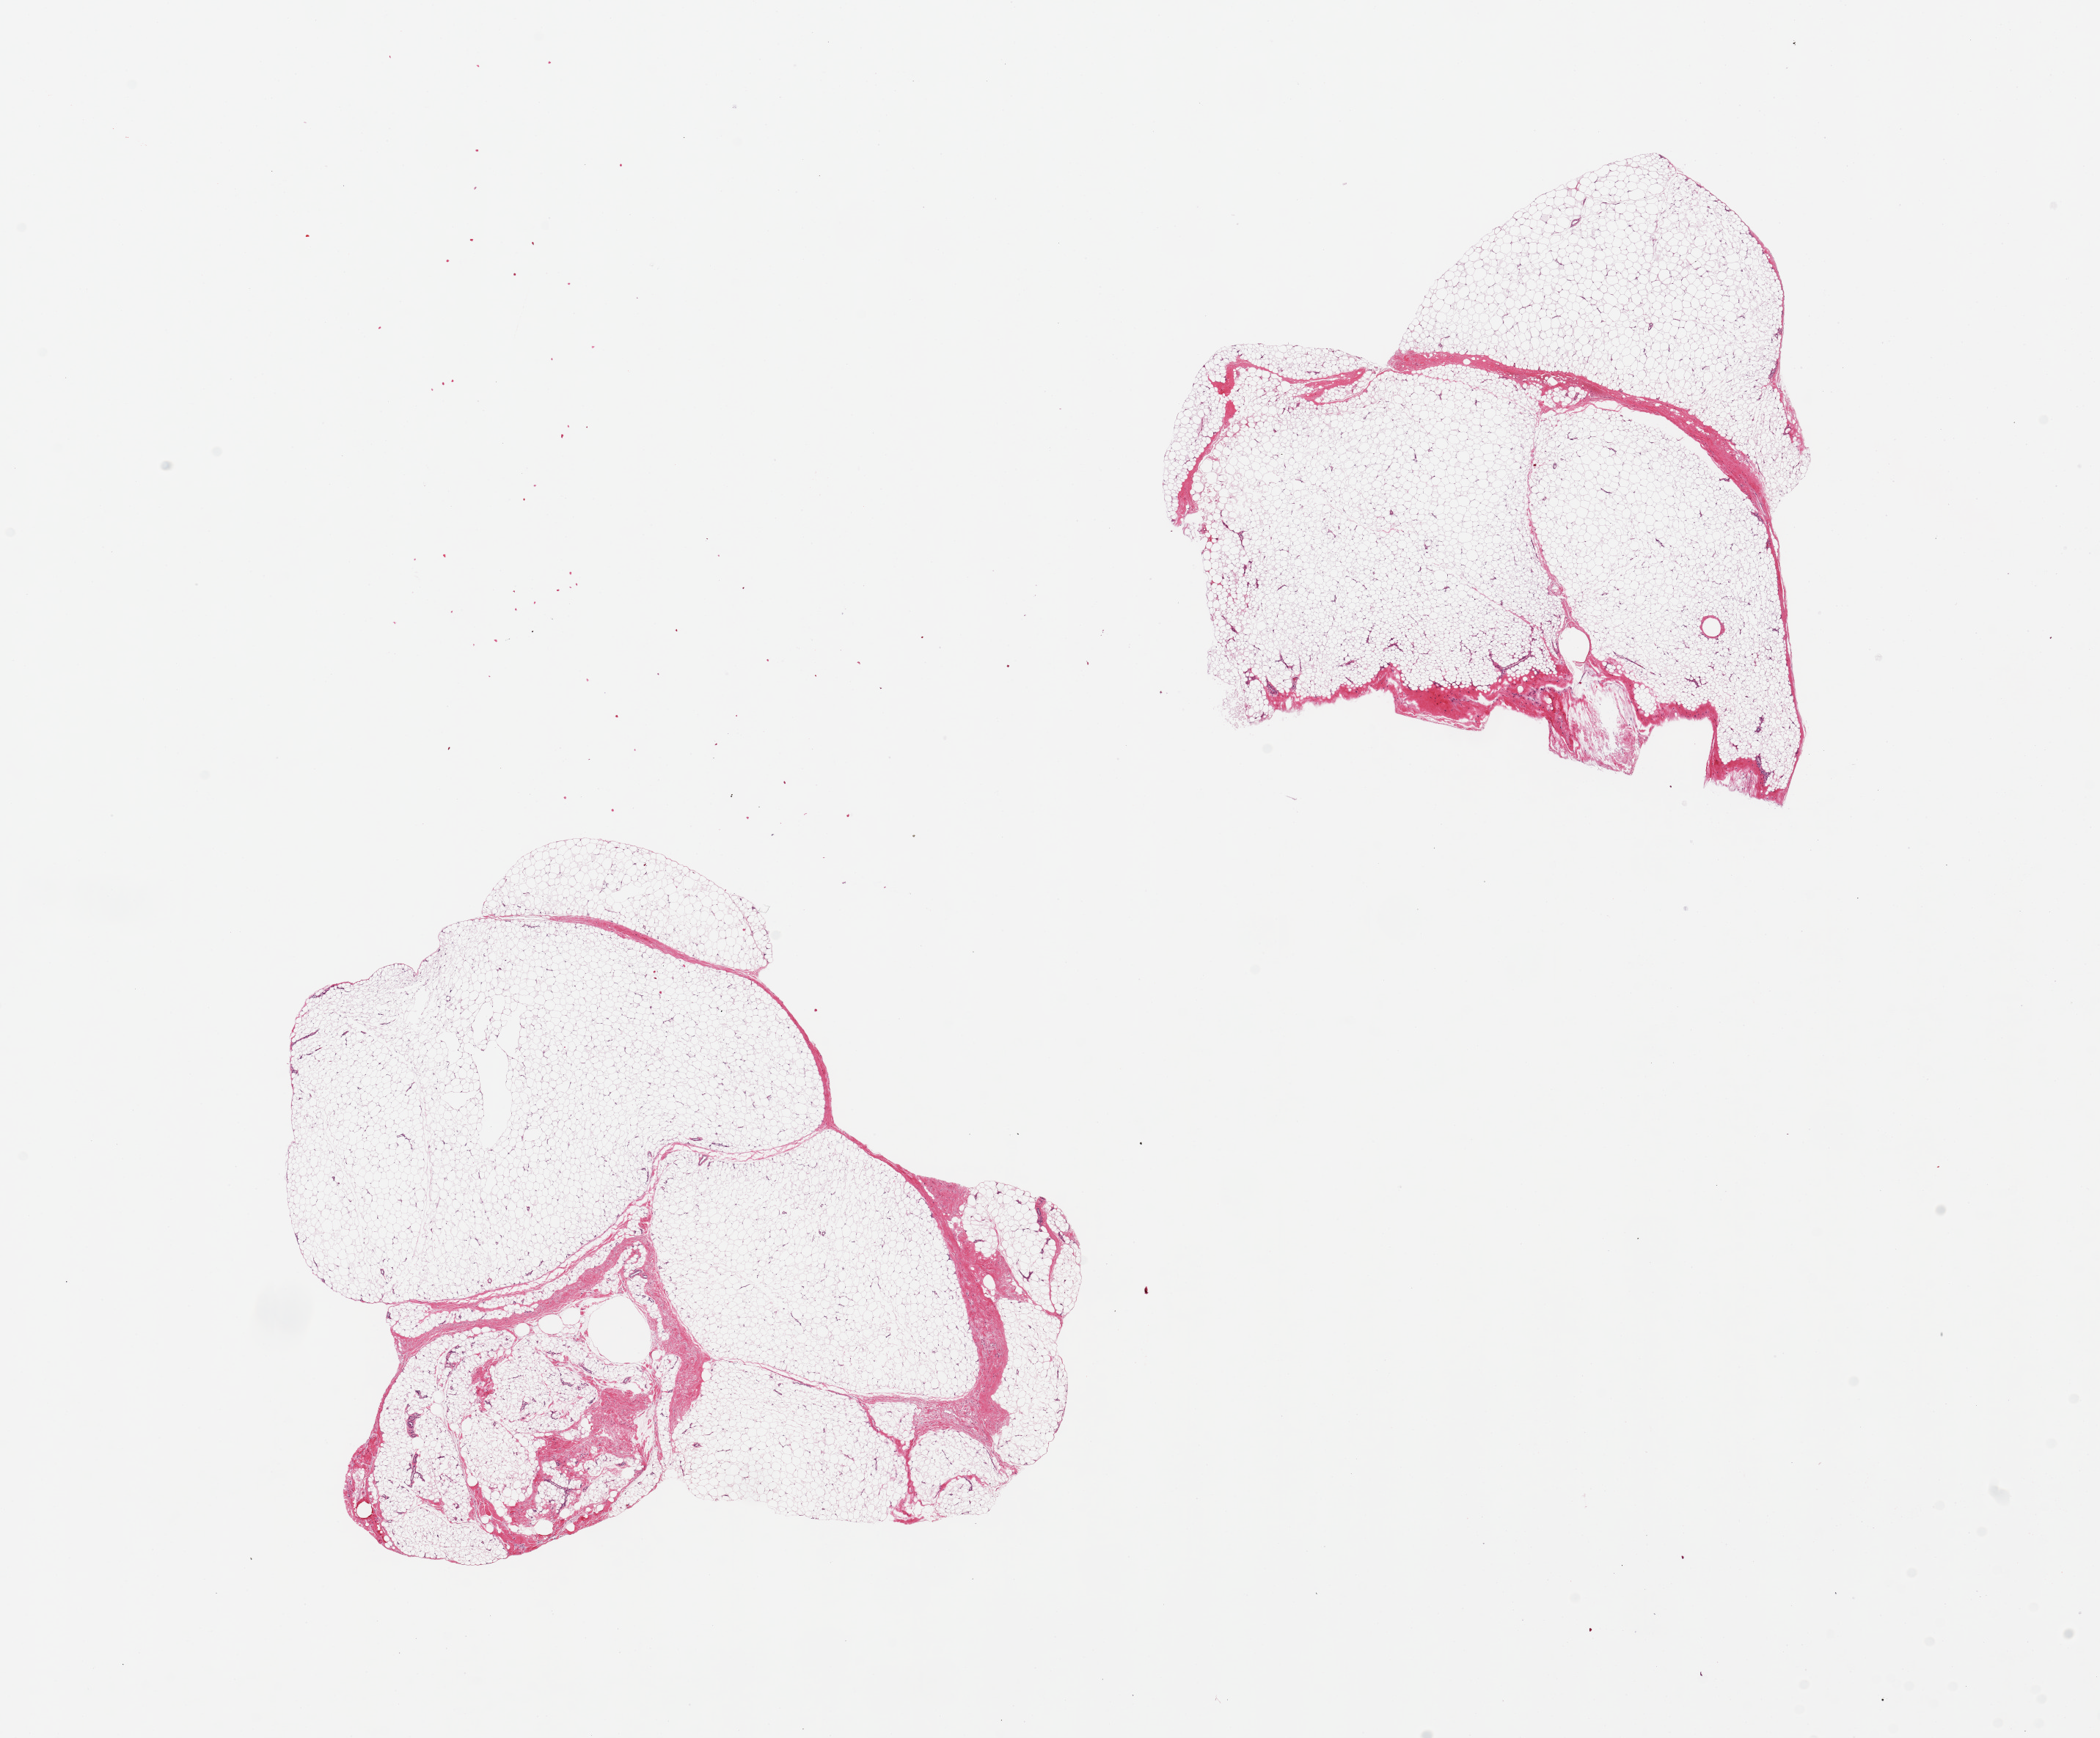
Haematoxylin and eosin whole-slide image, shown as a low-resolution overview of the whole scanned area (about 22.6 x 18.7 mm). PAXgene-fixed paraffin-embedded (PFPE) section. Sampled site (target tissue): adipose tissue. Donor tissue sample.
Review note (as recorded): 2 pieces, 9x8 & 8x7mm.